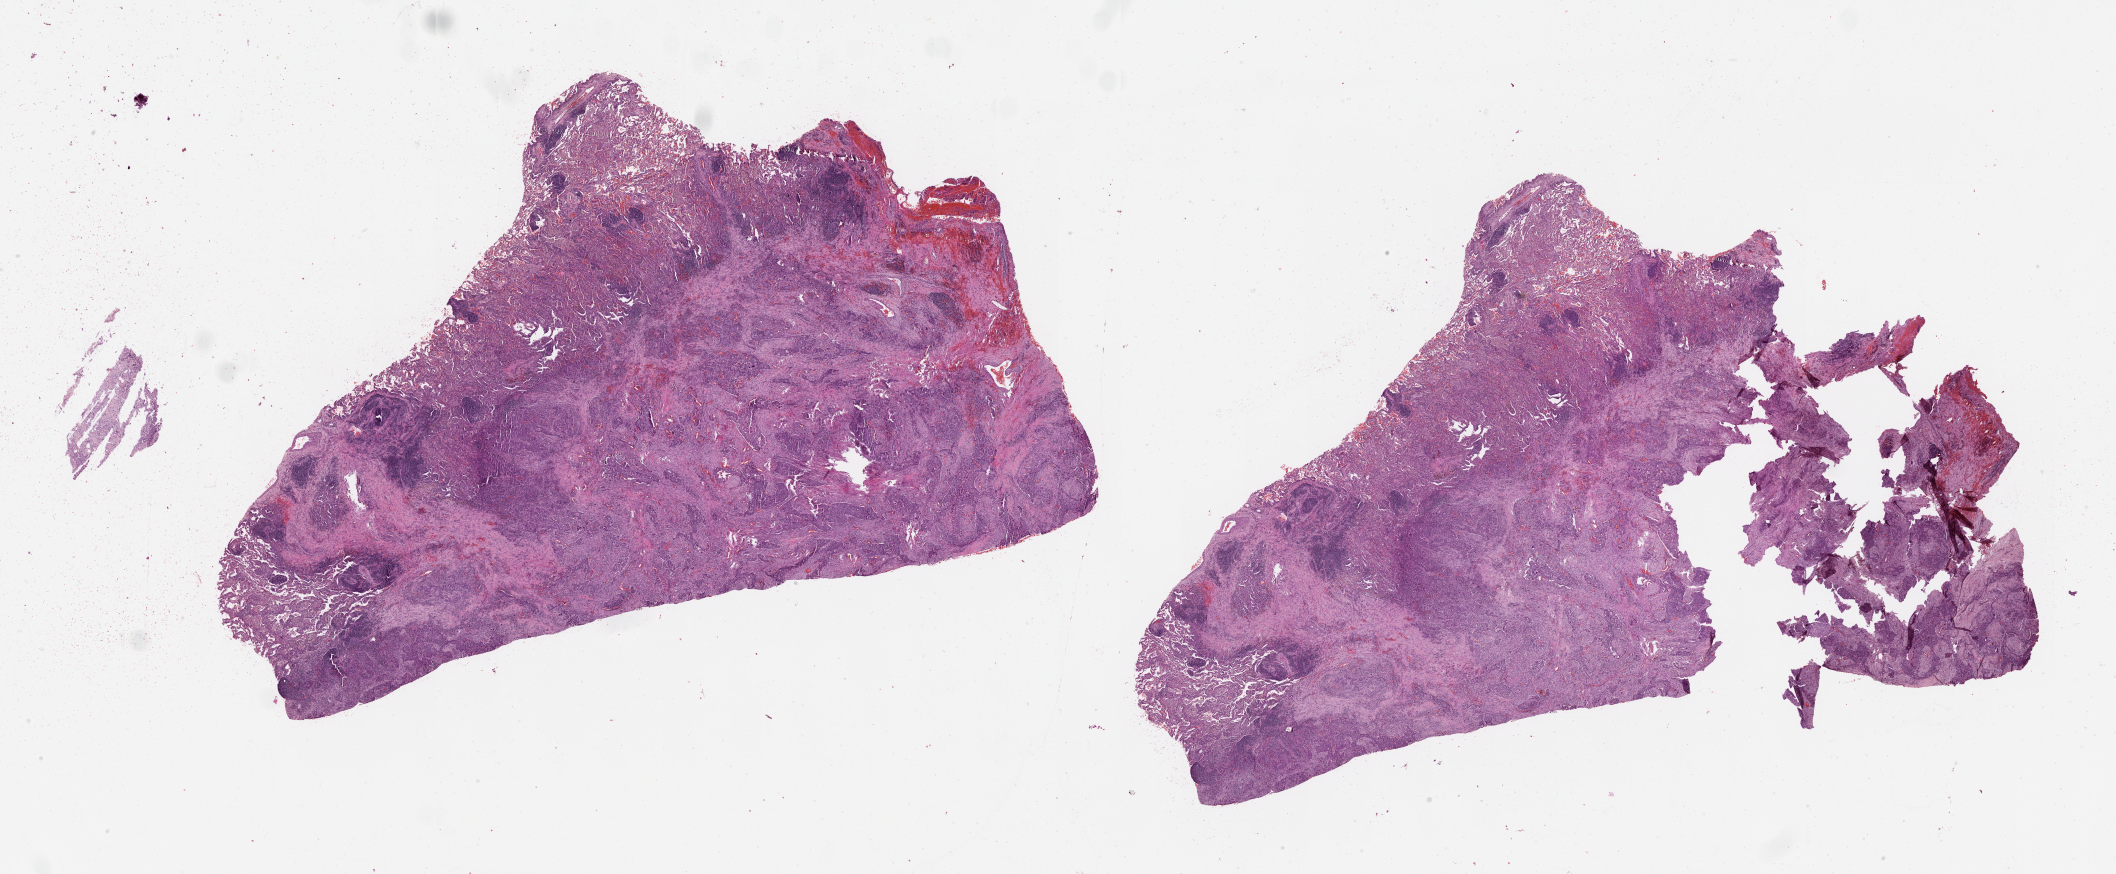
H&E-stained whole-slide image, whole scanned area (about 34.1 x 14.1 mm) shown as a low-resolution overview, tumour tissue sample, lung. 62-year-old female patient.
• patient diagnosis (cohort enrolment): squamous cell carcinoma (lung)